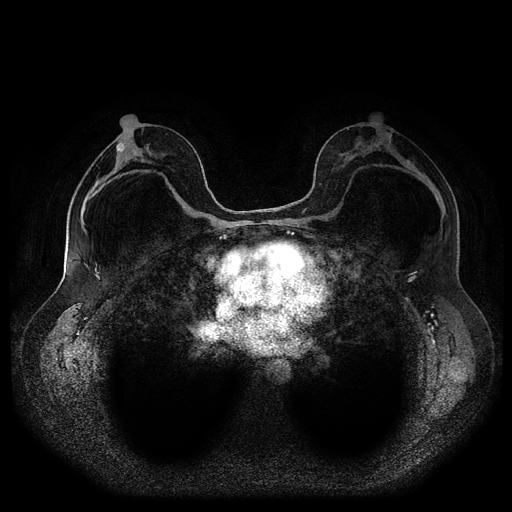
Breast MRI (dynamic contrast-enhanced, multi-phase), one axial slice. Slice 53 of 116 in the series (ordered by position). Dynamic contrast-enhanced series, time point 2 of 5 at this slice position (early post-contrast). 1.5 T. TE 2.6 ms, TR 5.3 ms. 2.2 mm slice thickness. 512 × 512 image matrix, field of view 360 × 360 mm. Female patient, age 46 years.
Outlined on this slice (semi-automatic segmentation, software-assisted and operator-edited):
- breast lesion (labelled 'tumour' in the annotation; benign lesions carry a separate 'benign' label): bounding box <116,143,125,151> (left, top, right, bottom; pixels)